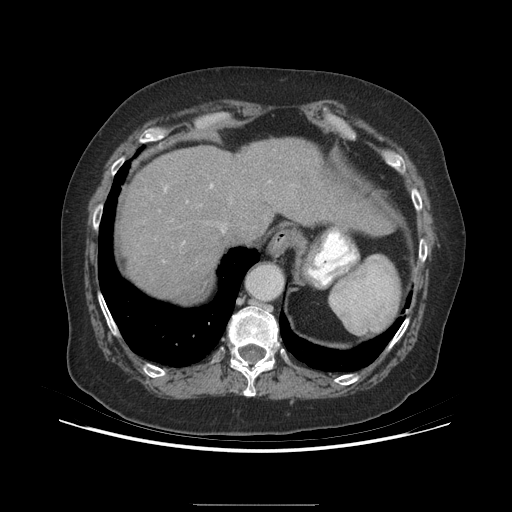
Contrast-enhanced abdominal CT (liver protocol), one axial slice. Slice 174 of 192 in the series (ordered by position). Reconstruction kernel STANDARD. 140 kVp. Soft-tissue window (W 400 / L 40 HU). 512 × 512 image matrix. From the clinical record (not read from this slice): diagnosis: hepatocellular carcinoma (patient treated with transarterial chemoembolisation; whether this scan precedes or follows treatment is not stated here); TNM stage (as recorded): Stage-I; Child-Pugh class: A; tumour differentiation: moderately differentiated; tumour nodularity: uninodular.
Annotated regions visible in this slice (semi-automatic segmentation, software-assisted and operator-edited):
- liver parenchyma outside the tumour (the mass and vessels are separate outlines, so this box may not span the whole liver): bounding box [x1, y1, x2, y2] px = [120, 138, 392, 300]